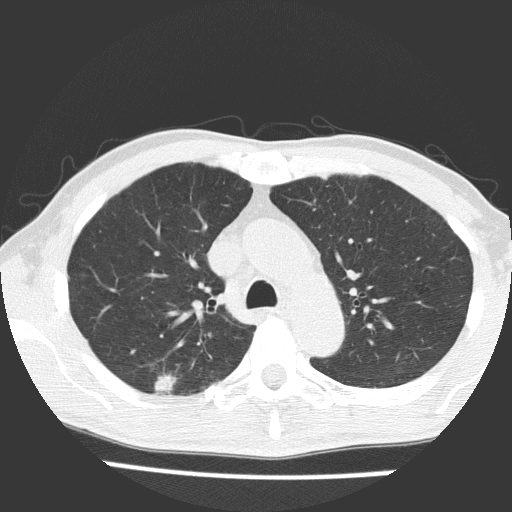
Axial slice from a low-dose chest CT screening exam, baseline annual screen, lung window (W 1500 / L -600 HU), 2 mm slice thickness, lung (sharp) reconstruction kernel (FC51), 120 kVp. Male participant, aged 66 years at enrolment. Current smoker at enrolment.
Expert reader's lesion annotation, box from (x=139, y=359) to (x=193, y=410) px. Reader record for this screening exam (exam-level; its link to the box is not recorded): non-calcified nodule or mass ≥4 mm, right upper lobe, 15 × 10 mm, spiculated (stellate) margins, soft tissue attenuation. Lung cancer was diagnosed 43 days after this screen: adenocarcinoma, NOS, right upper lobe, moderately differentiated (G2), stage IB (AJCC 6th edition), 11 mm at pathology.